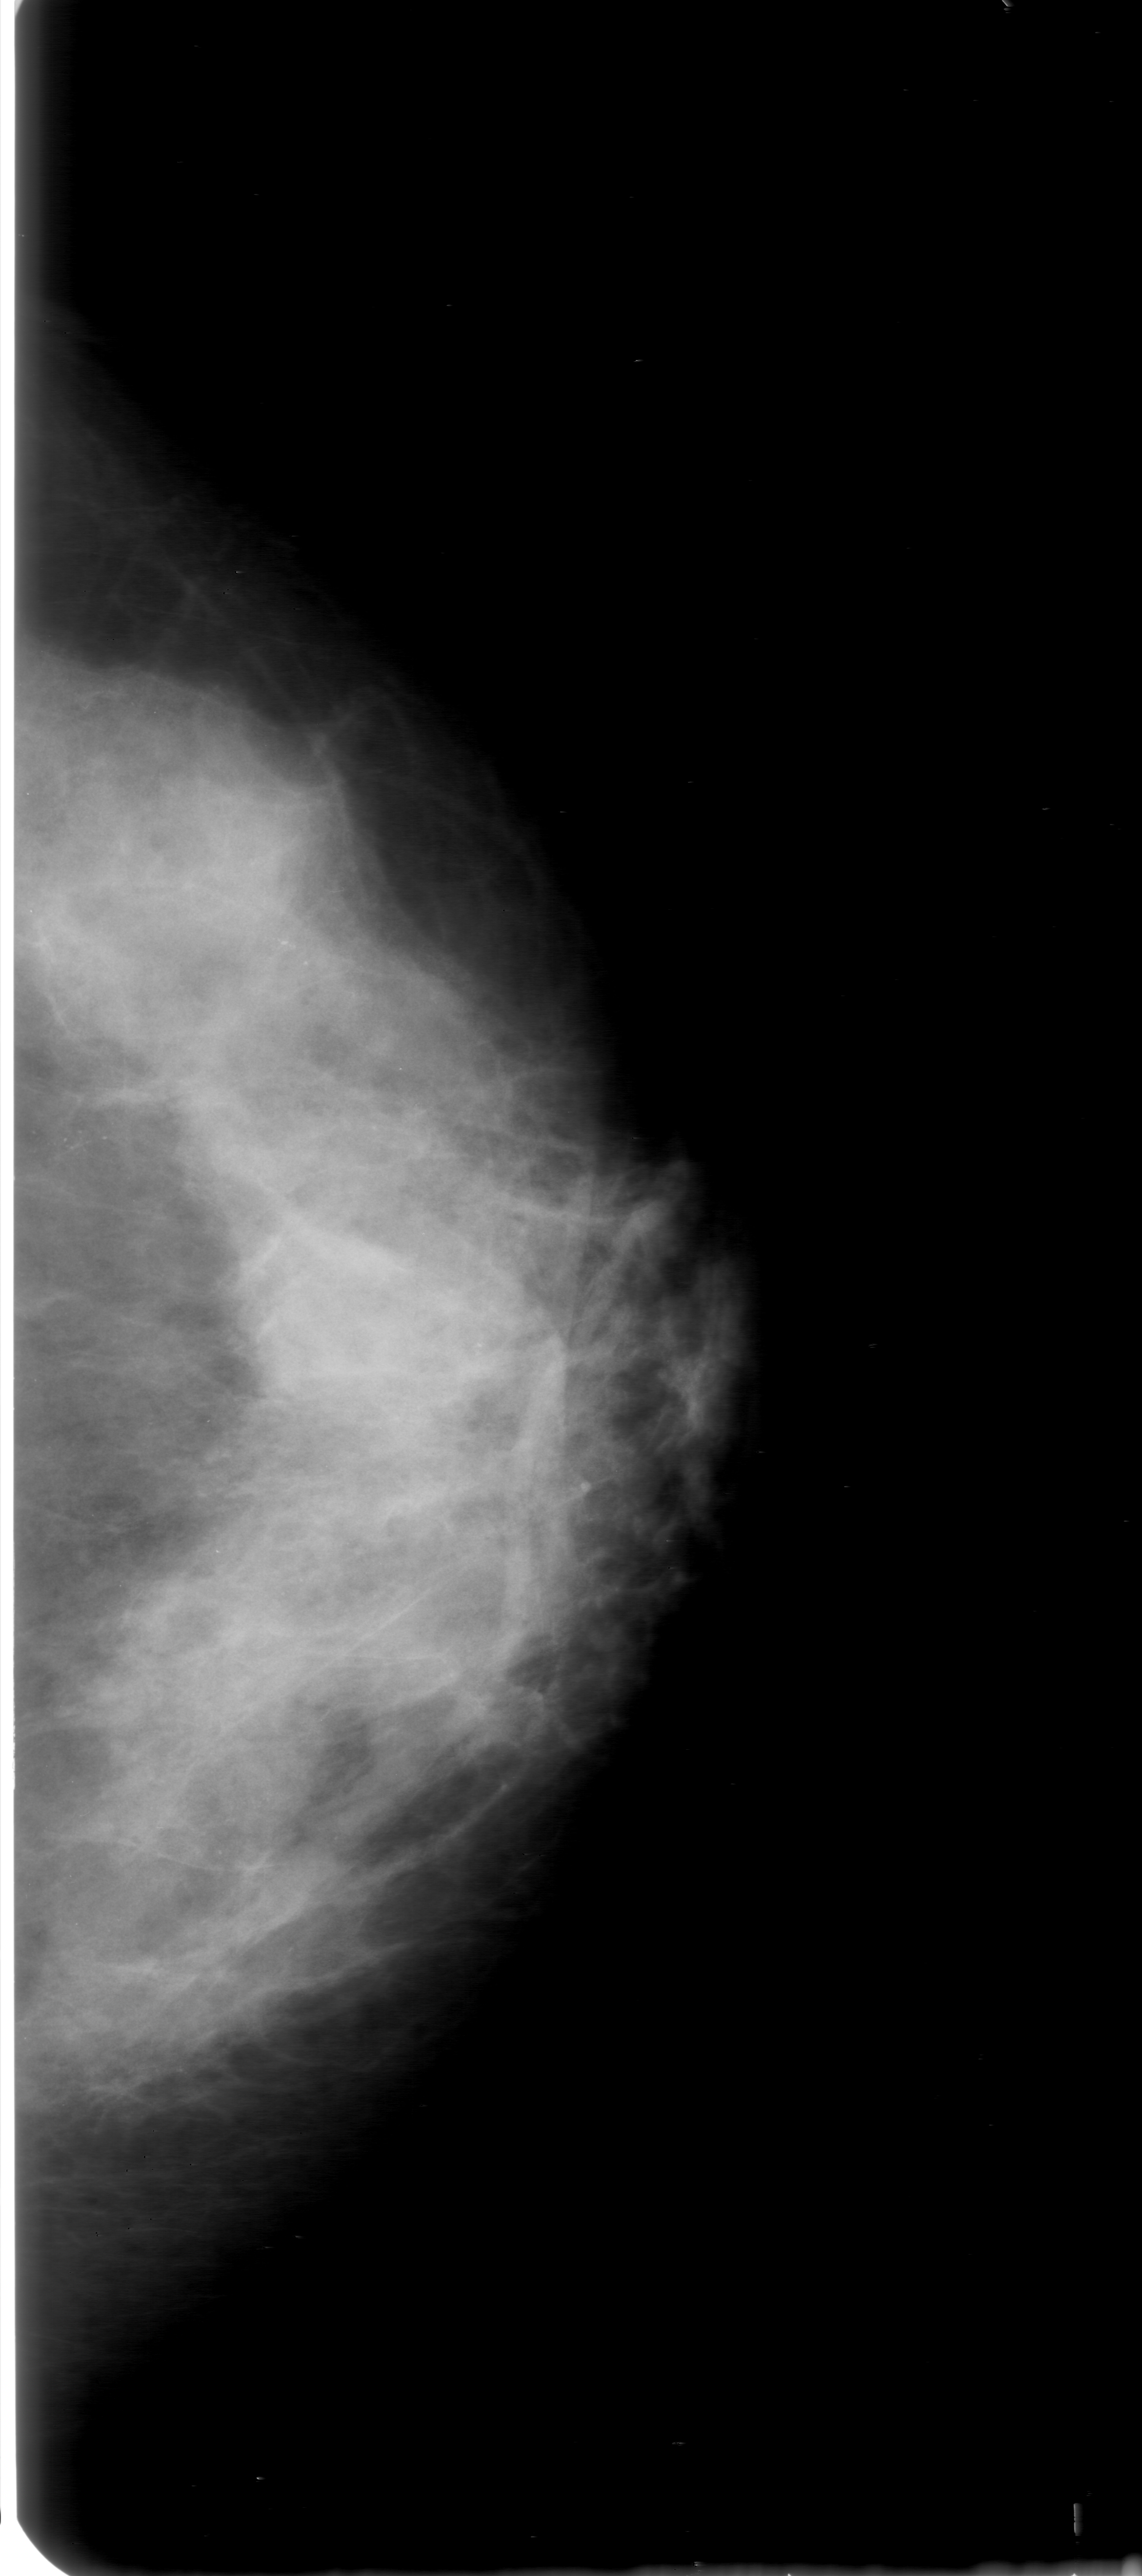
Scanned film-screen mammogram; left breast; craniocaudal (CC) view.
- Calcifications, morphology pleomorphic, distribution clustered; BI-RADS assessment category 0 (incomplete: needs additional imaging); subtlety rating 3 on a 1 (subtle) to 5 (obvious) scale; pathology result (as recorded, not read from the image): malignant.